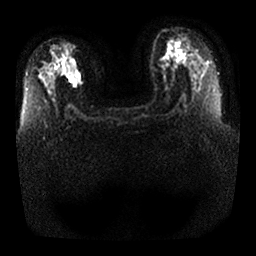
Breast MRI, one axial slice. Position 14 of 25 along the scan axis. Diffusion-weighted series; image 2 of 4 stored at this slice position (different b-values; order by instance number). 1.5 T. 4 mm slice thickness. 256 × 256 image matrix, field of view 350 × 350 mm. Female patient.
Outlined on this slice (expert manual segmentation):
- tumour on diffusion-weighted imaging: bounding box [x1, y1, x2, y2] px = [63, 62, 80, 82]